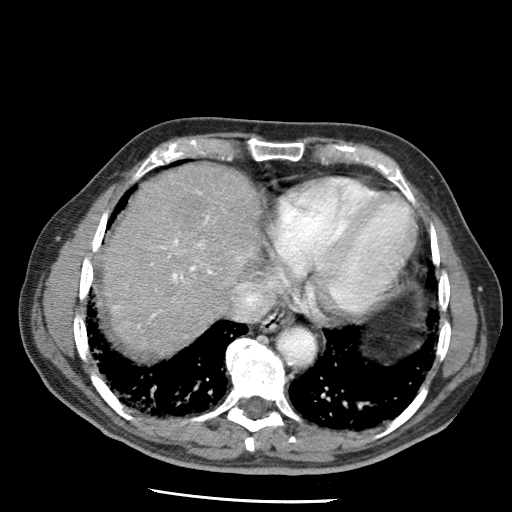
Contrast-enhanced abdominal CT (liver protocol), one axial slice. Soft-tissue window (W 400 / L 40 HU). 512 × 512 image matrix, field of view 320 × 320 mm. Case-level facts recorded for this patient, not image findings: diagnosis: hepatocellular carcinoma (patient treated with transarterial chemoembolisation; whether this scan precedes or follows treatment is not stated here); TNM stage (as recorded): Stage-IIIA.
Outlined on this slice (semi-automatically segmented with operator editing):
- liver parenchyma outside the tumour (the mass and vessels are separate outlines, so this box may not span the whole liver): bounding box [x1, y1, x2, y2] px = [102, 164, 260, 356]
- liver vessels: [114, 190, 252, 328]